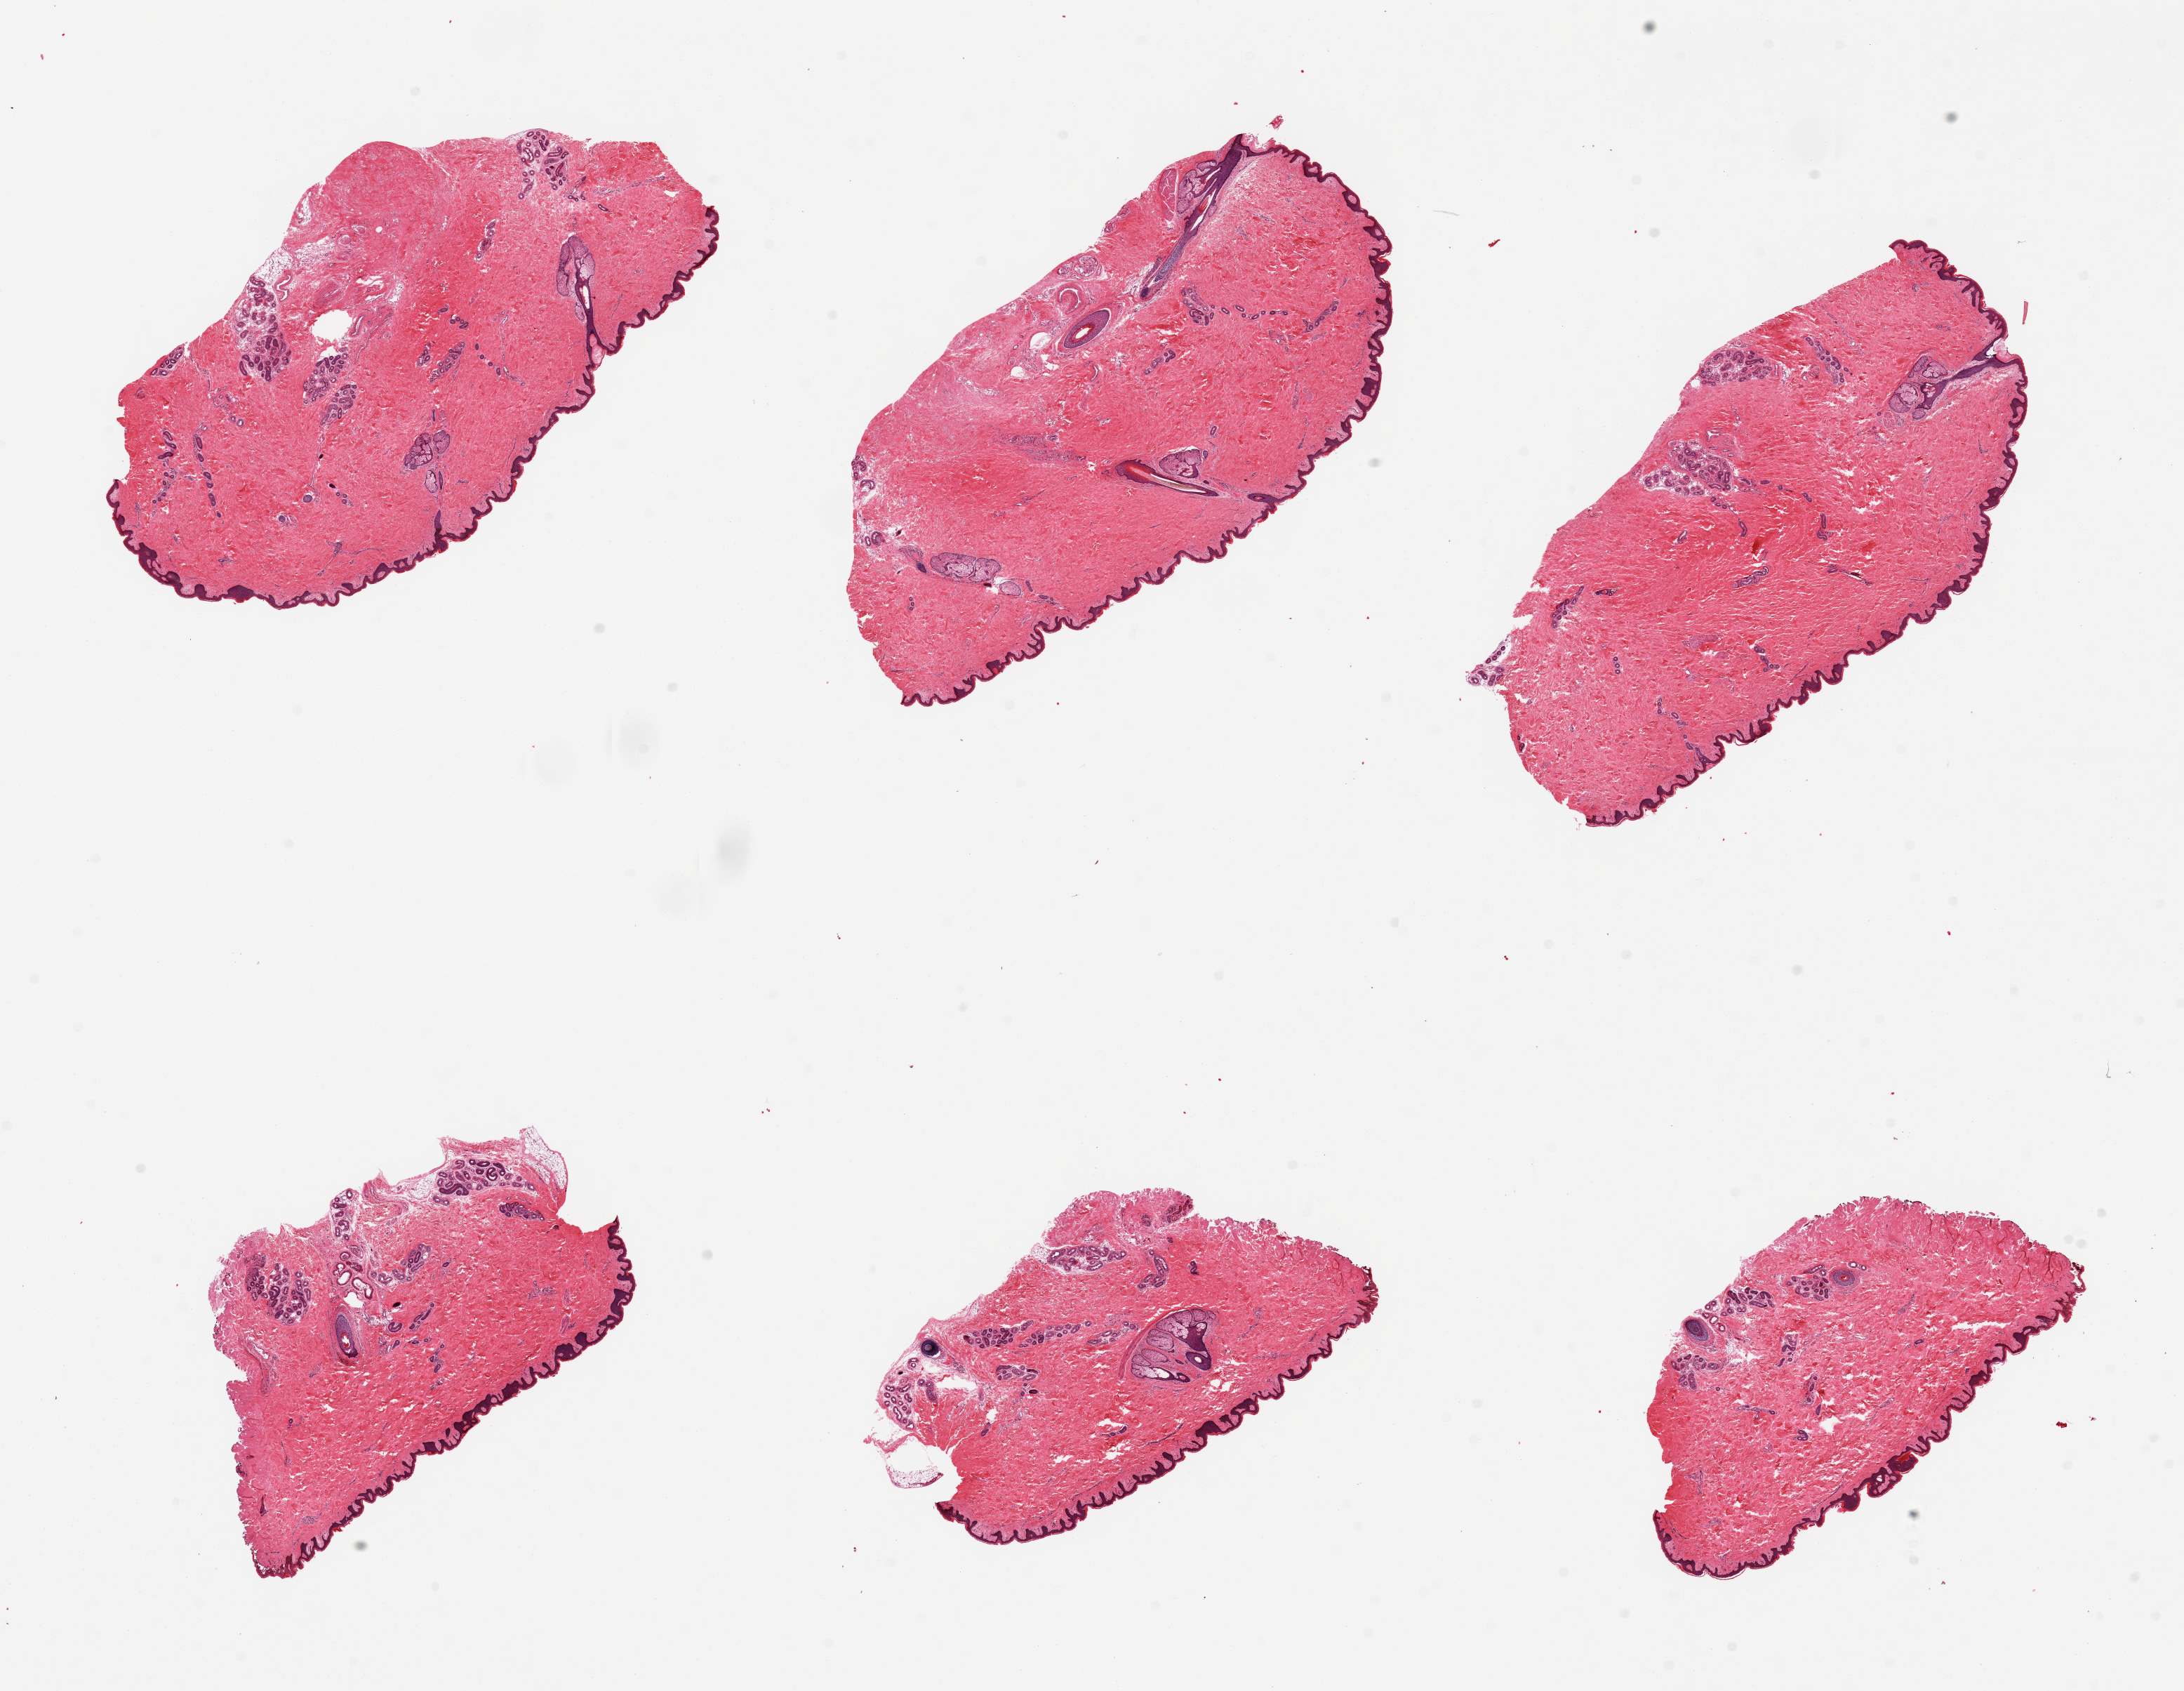
Haematoxylin and eosin whole-slide image, brightfield — a low-resolution overview of the entire scanned area, about 24.6 x 19.1 mm (slide scanned at 20x). PAXgene-fixed, paraffin-embedded tissue. Sampled site (target tissue): skin of suprapubic region. Tissue donor sample. Male donor.
* review note (as recorded): 6 pieces; well trimmed